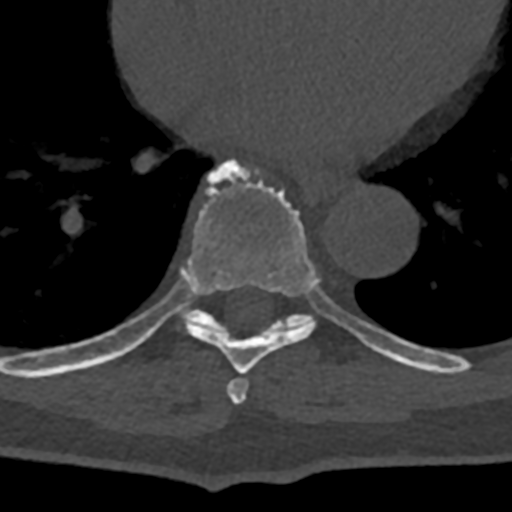
CT including the spine, one axial slice; slice 695 of 797 in the series (ordered by position); reconstruction kernel Br40s/3; 120 kVp; bone window (W 1800 / L 400 HU); 0.5 mm slice thickness; 512 × 512 image matrix, field of view 160 × 160 mm. Patient: male, 74 years. From the clinical record (not read from this slice): primary cancer: renal; vertebrae with lytic lesions (as recorded): T10, L1, L2, L3, L4, L5.
Structures marked on this image (semi-automatic segmentation, software-assisted and operator-edited):
- T7 vertebra: bounding box (x1, y1, x2, y2) in pixels: (227, 378, 248, 404)
- T8 vertebra: (70, 159, 399, 374)
- T9 vertebra: (168, 272, 432, 371)